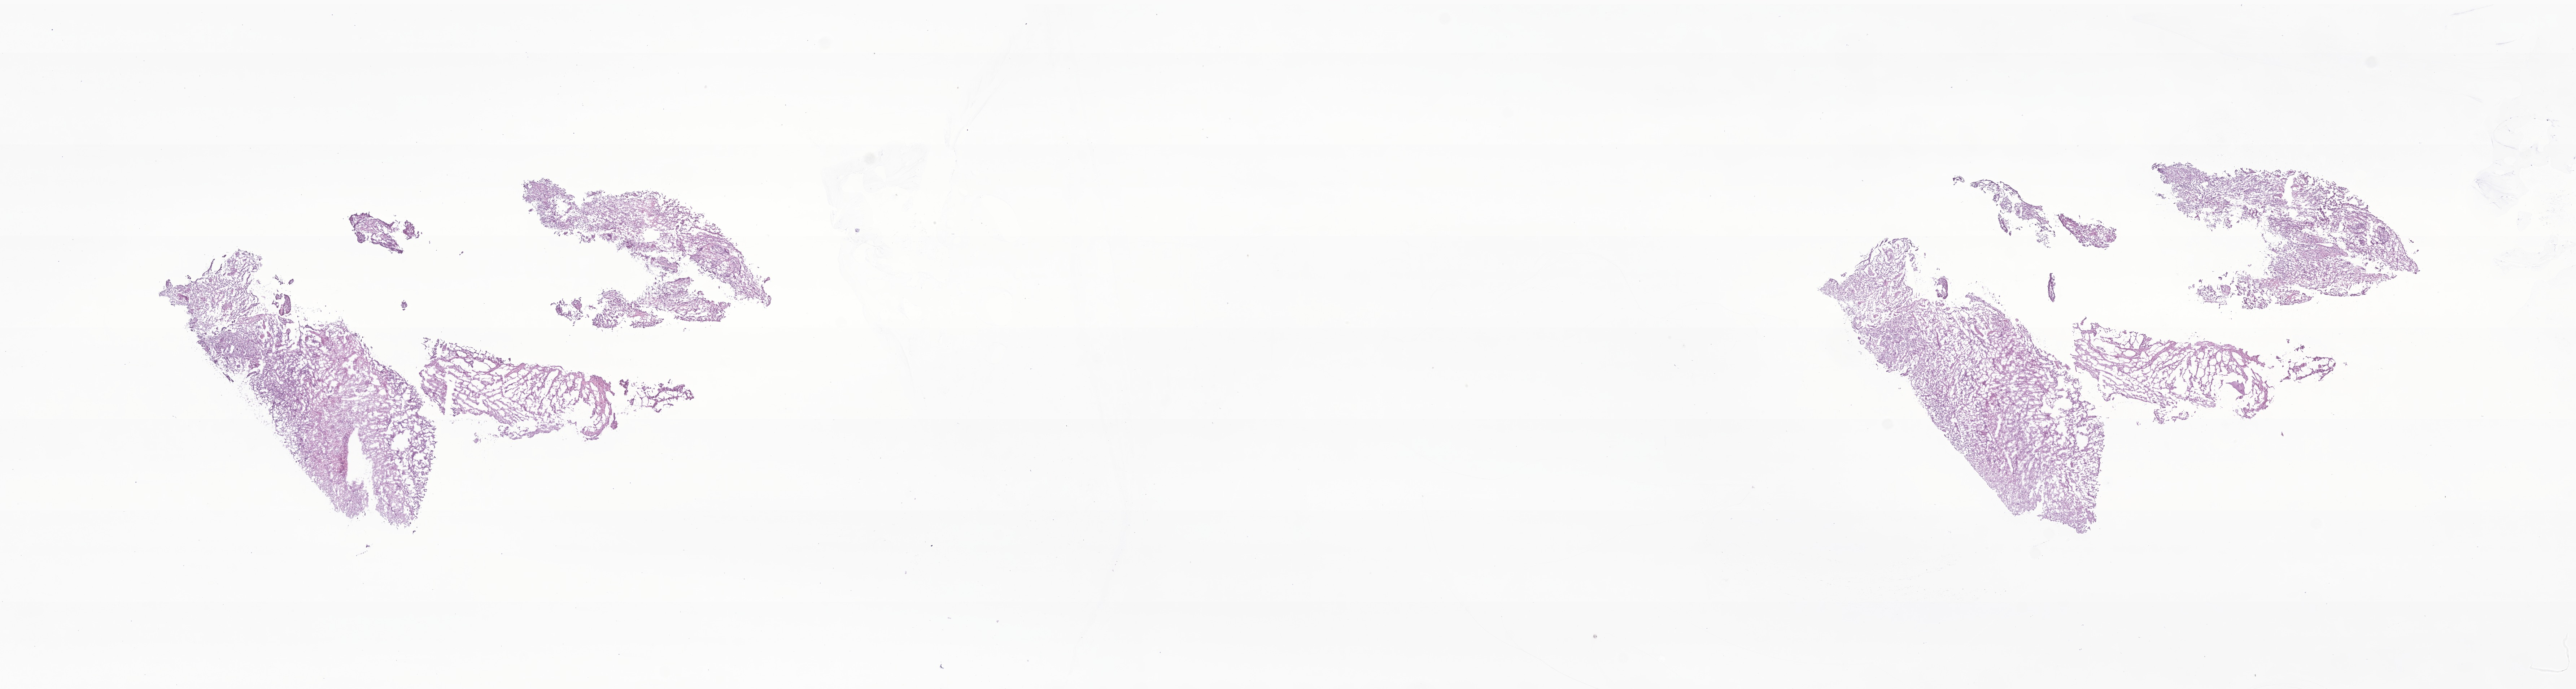
Hematoxylin and eosin (H&E) whole-slide image of tumor tissue from the occipital lobe — low-resolution overview of the scanned area, about 30.1 x 8.0 mm, cryosection (OCT / tissue freezing medium). Patient female; age 73 months.
Diagnosis (ICD-O-3 morphology term): Ependymoma, NOS.